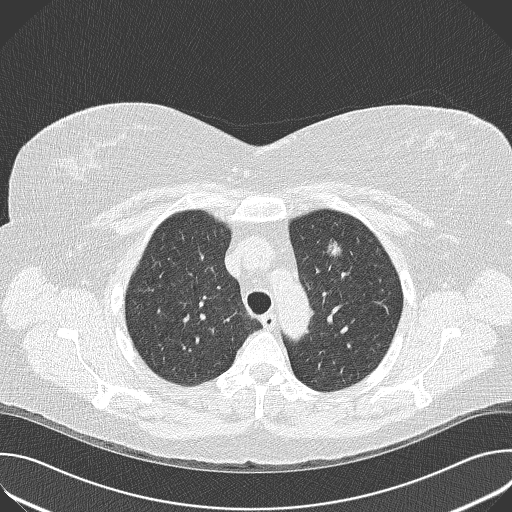
Low-dose screening chest CT, axial slice; baseline annual screen; lung window (W 1500 / L -600 HU); lung (sharp) reconstruction kernel (B50f); slice 112 of 143 in the series. Female participant, aged 57 years at enrolment. Current smoker at enrolment.
Lesion marked by an expert reader, bounding box <315,234,351,270> (left, top, right, bottom; pixels). The screening reader recorded 3 non-calcified nodules or masses ≥4 mm on this exam; which of them this box marks is not recorded. Official screen result: positive, change unspecified: nodule(s) >= 4 mm or enlarging nodule(s), mass(es), or other non-specific abnormalities suspicious for lung cancer. Lung cancer was diagnosed 446 days after this screen: adenocarcinoma, NOS, left upper lobe, poorly differentiated (G3), stage IA (AJCC 6th edition), 24 mm at pathology.